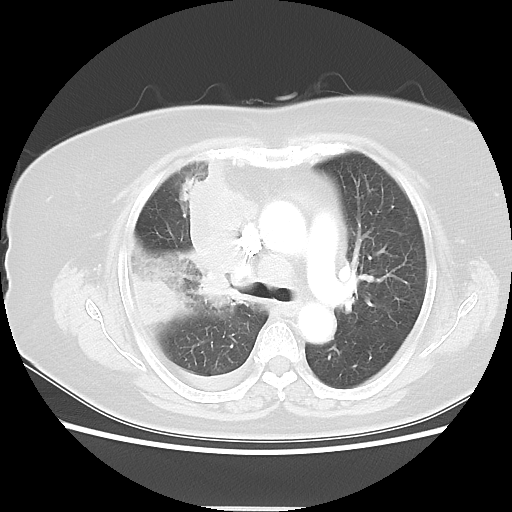
Chest CT, one axial slice. Slice 31 of 48 in the series (ordered by position). Reconstruction kernel LUNG. 120 kVp. Lung window (W 1500 / L -600 HU). 5 mm slice thickness. 512 × 512 image matrix. Patient: female, 73 years. Case-level facts recorded for this patient, not image findings: clinical TNM (as recorded): T3 N3 M1b; histopathological grade: G3.
Structures marked on this image (bounding box drawn by a radiologist):
- lung tumour (recorded histology: small cell carcinoma): bounding box <179,149,260,298> (left, top, right, bottom; pixels)